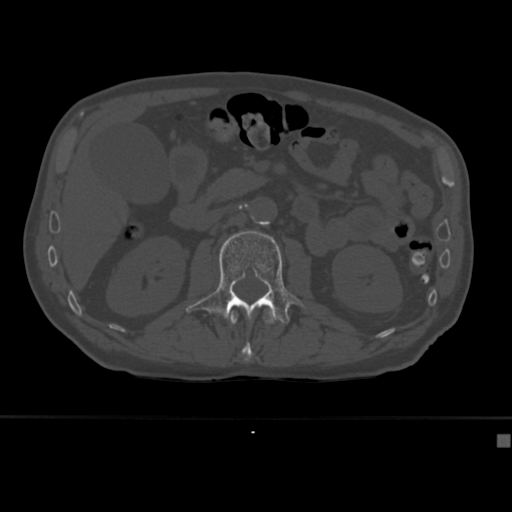
CT including the spine, one axial slice. Slice 152 of 430 in the series (ordered by position). Reconstruction kernel Br40s. 120 kVp. Bone window (W 1800 / L 400 HU). 1.5 mm slice thickness. 512 × 512 image matrix, field of view 337 × 337 mm. Male patient, age 64 years. From the clinical record (not read from this slice): primary cancer: uterus.
Annotated regions visible in this slice (semi-automatic segmentation, software-assisted and operator-edited):
- L1 vertebra: bounding box (x1, y1, x2, y2) in pixels: (229, 308, 276, 362)
- L2 vertebra: (186, 230, 304, 324)